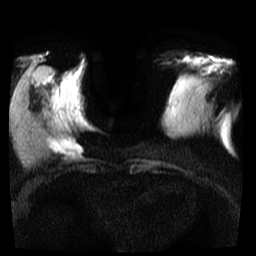
Breast MRI, one axial slice; position 10 of 35 along the scan axis; diffusion-weighted series; image 2 of 4 stored at this slice position (different b-values; order by instance number); 3 T; 5 mm slice thickness; 256 × 256 image matrix, field of view 300 × 300 mm. Female patient.
Outlined on this slice (expert manual segmentation):
- tumour on diffusion-weighted imaging: bounding box [x1, y1, x2, y2] px = [48, 137, 83, 156]